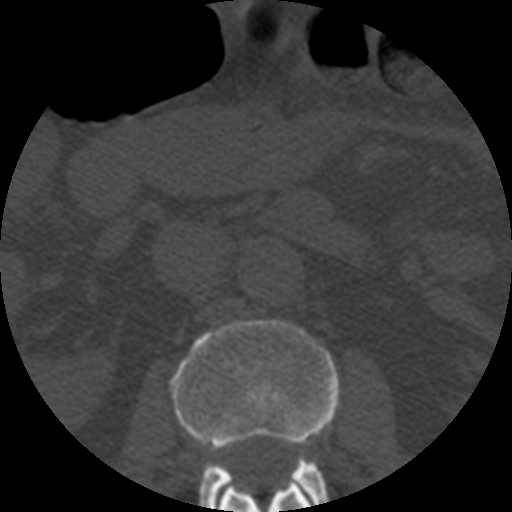
CT including the spine, one axial slice. Slice 165 of 508 in the series (ordered by position). Reconstruction kernel STANDARD. Bone window (W 1800 / L 400 HU). 1.25 mm slice thickness. 512 × 512 image matrix. Patient age 57 years. Case-level facts recorded for this patient, not image findings: primary cancer: prostate.
Annotated regions visible in this slice (semi-automatically segmented with operator editing):
- L1 vertebra: bounding box [x1, y1, x2, y2] px = [219, 481, 313, 512]
- L2 vertebra: [170, 320, 339, 512]